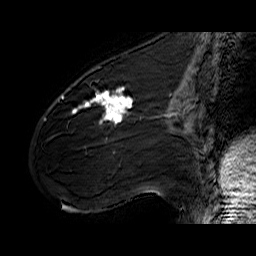
Breast MRI (dynamic contrast-enhanced), one sagittal slice; position 23 of 60 along the scan axis; dynamic contrast-enhanced series, time point 2 of 6 at this slice position (early post-contrast); 1.5 T; TE 6.4 ms, TR 32.9 ms; 4 mm slice thickness; 256 × 256 image matrix, field of view 200 × 200 mm. Female patient. From the clinical record (not read from this slice): setting: breast cancer imaged before/during neoadjuvant chemotherapy; receptor status: HER2-positive.
Structures marked on this image (semi-automatic segmentation, software-assisted and operator-edited):
- analysis volume of interest (the breast-tissue region the enhancement analysis was run in; not a lesion): bounding box (x1, y1, x2, y2) in pixels: (61, 77, 141, 142)
- tumour enhancement mask (voxels above the 100 % enhancement threshold inside the analysis volume of interest): (61, 87, 134, 126)